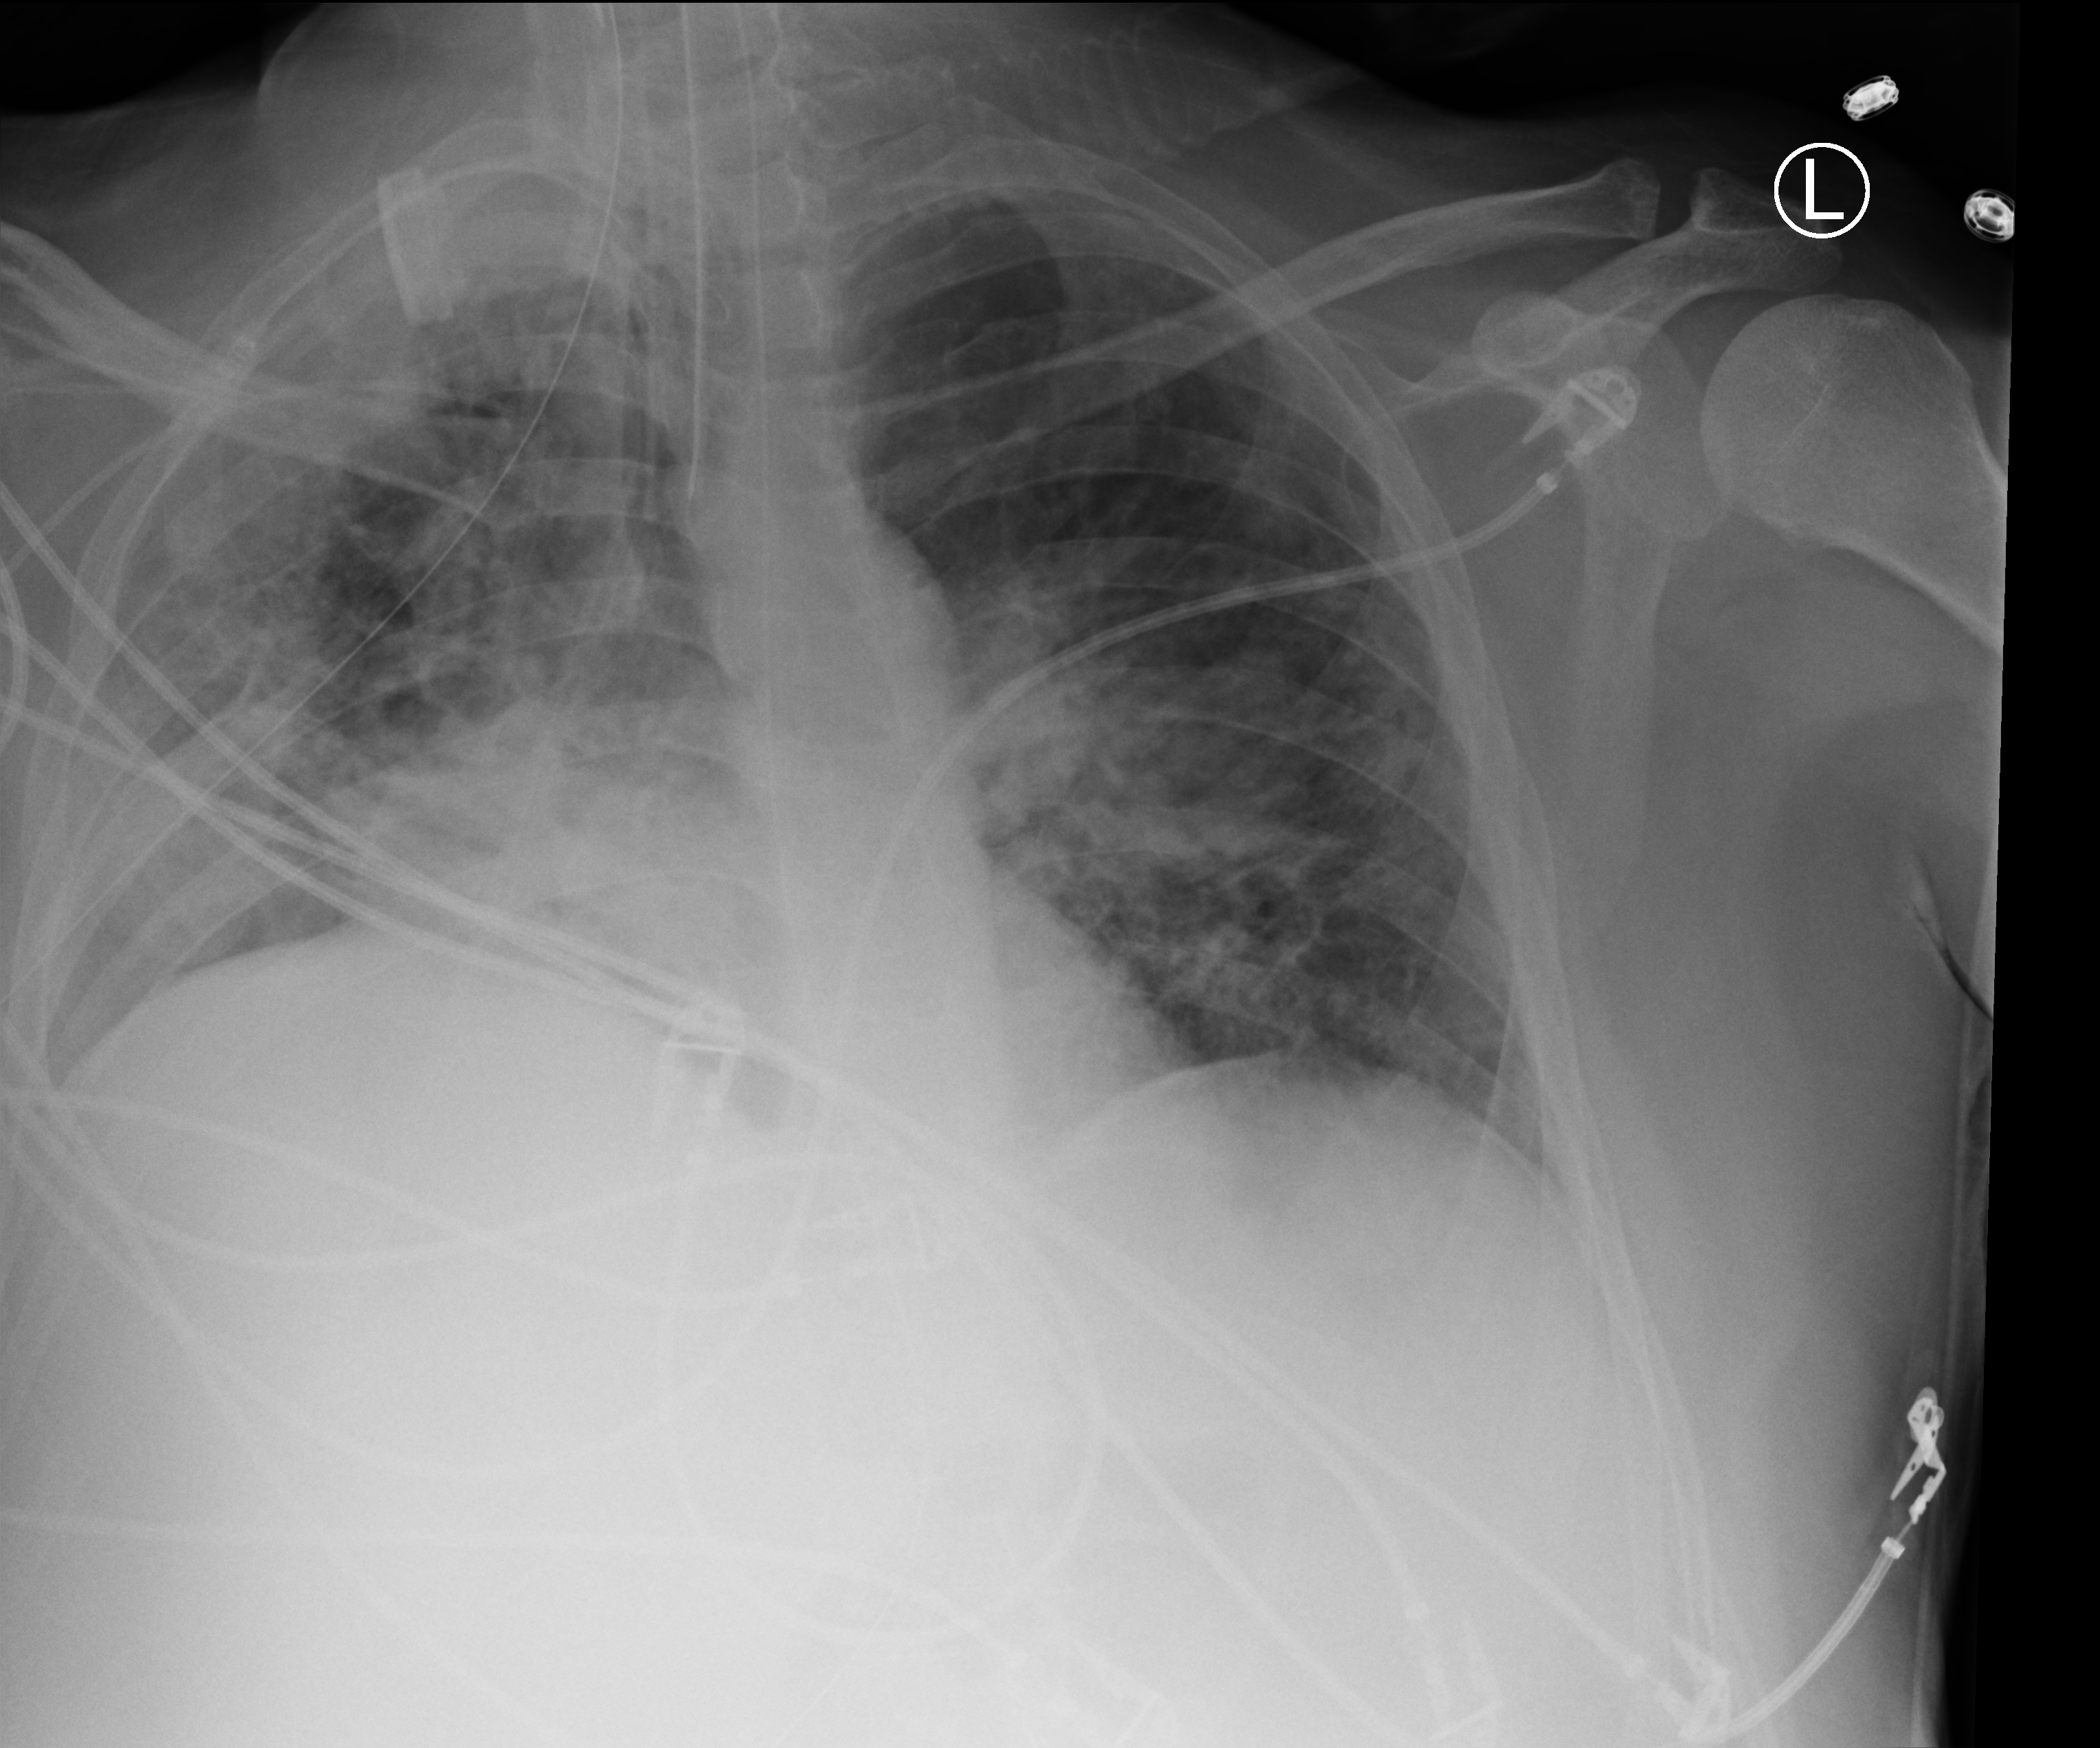
Bedside chest radiograph (computed radiography); anteroposterior (AP) projection. Patient hospitalised with COVID-19, aged 18–59 years.
From the hospital-stay record, not from the radiograph (when in the stay this image was taken is not recorded): diabetes (admission record): no.